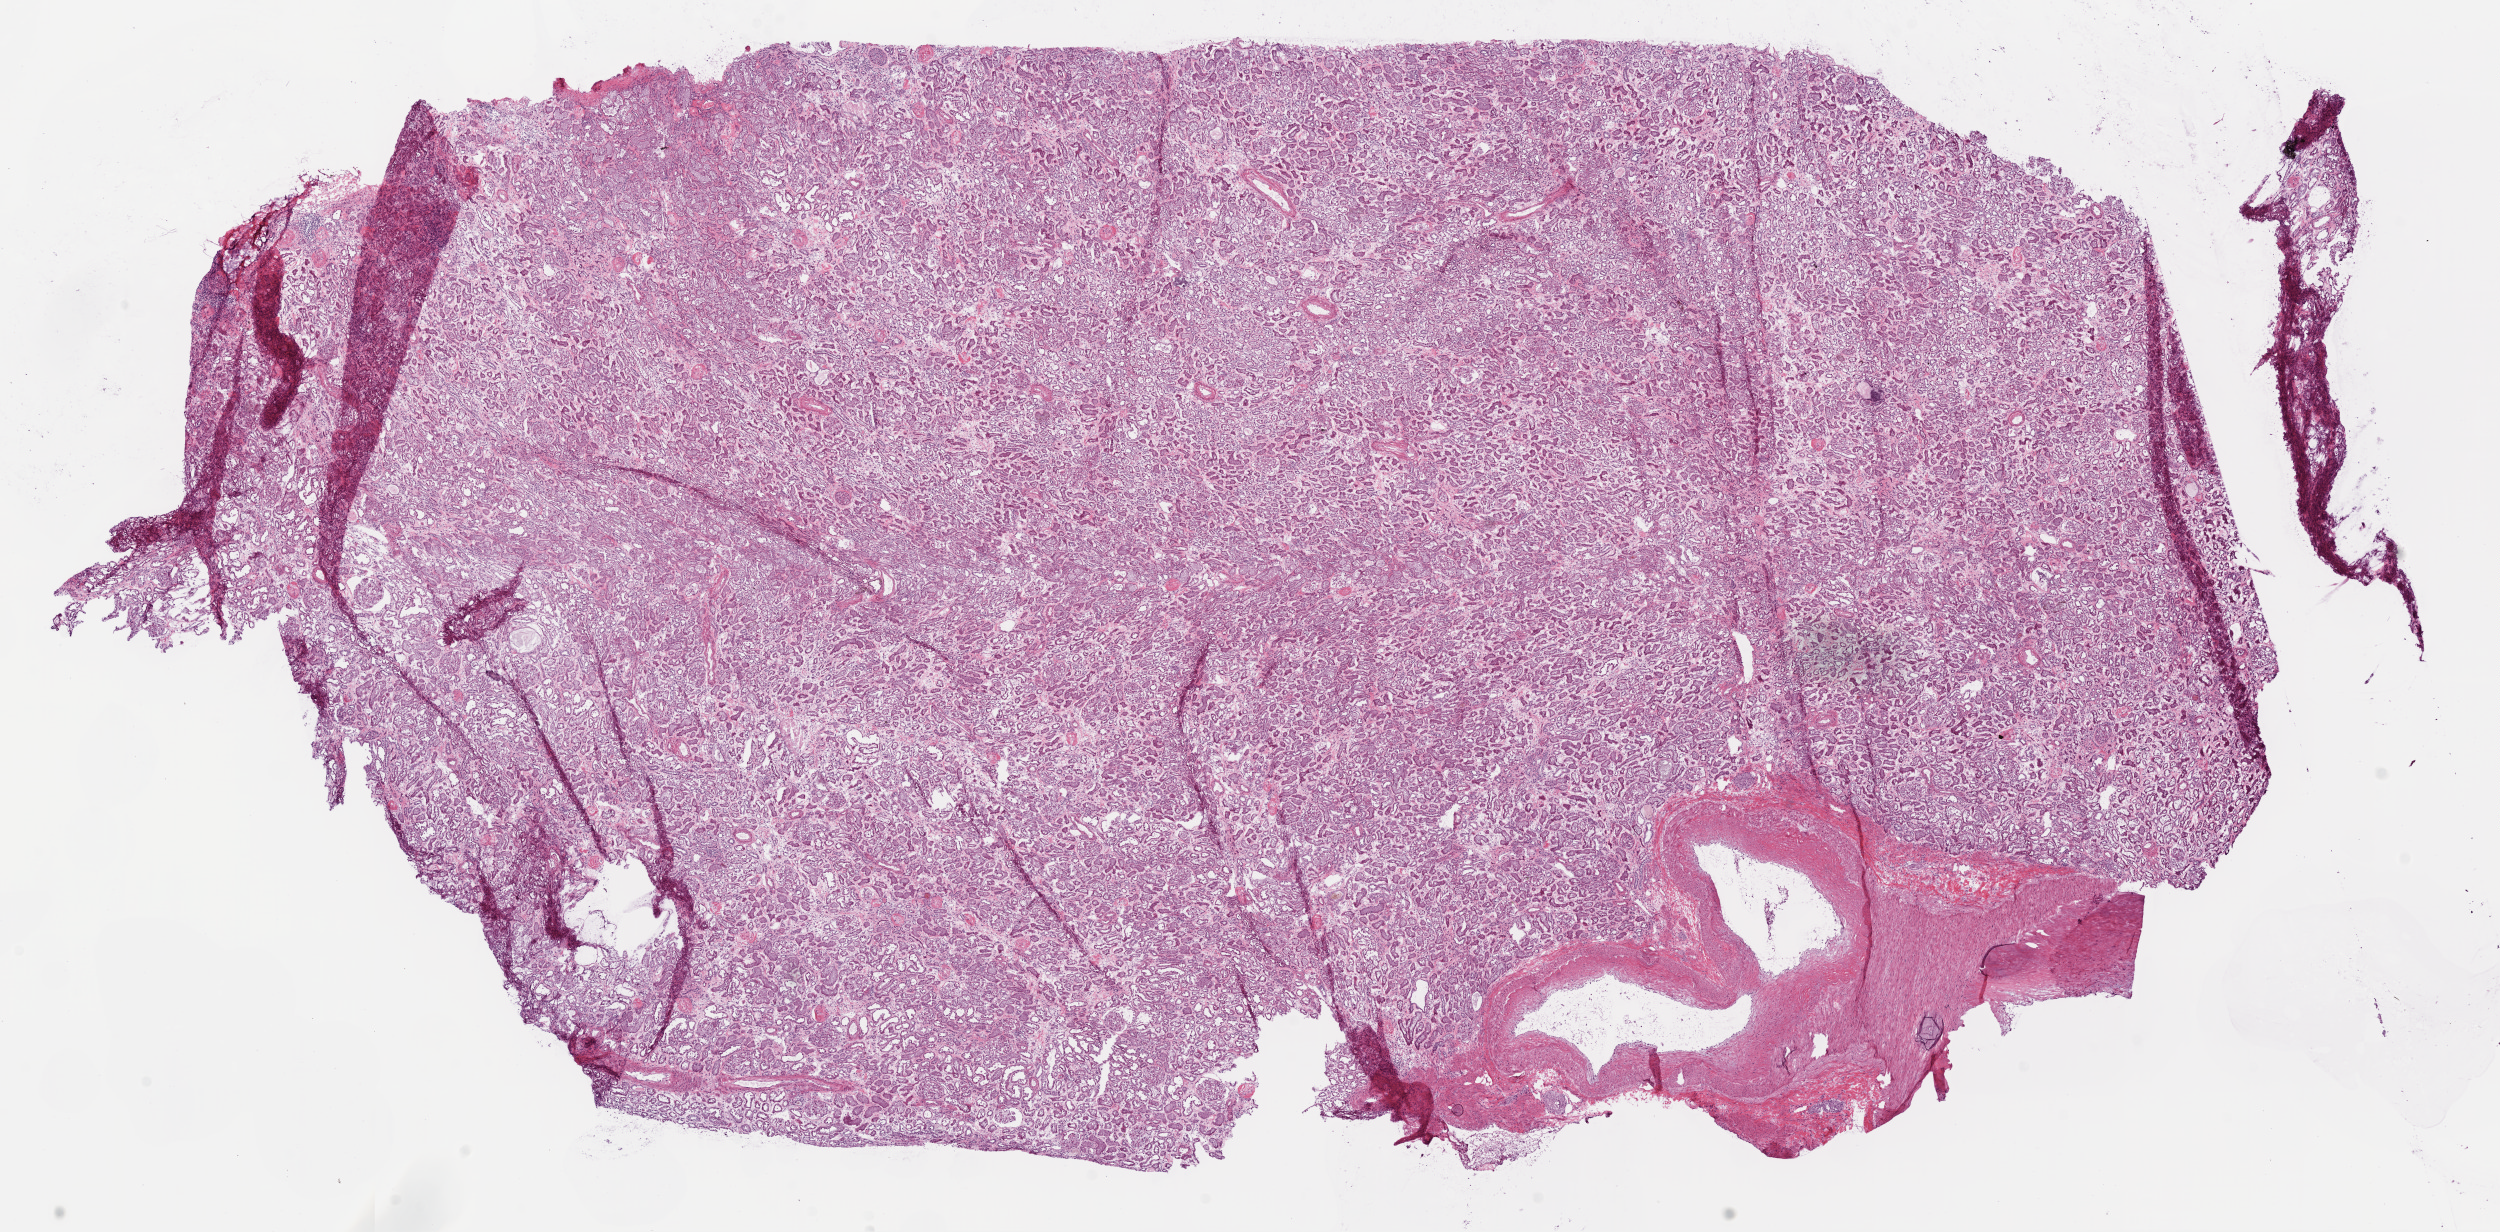
Hematoxylin and eosin (H&E) stained whole-slide image — a low-resolution overview of the entire scanned area, about 20.1 x 9.9 mm (acquisition: 20x scan). Frozen section. Solid tissue normal (non-tumour tissue) sample from the kidney. Male, age 83 years at initial diagnosis.
* this section: solid tissue normal (non-tumour) sample from the same patient
* patient diagnosis: Clear cell adenocarcinoma, NOS